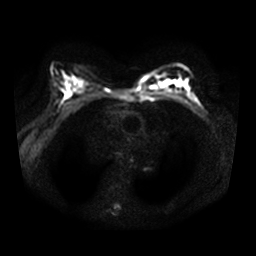
Breast MRI, one axial slice; position 19 of 32 along the scan axis; diffusion-weighted series; image 2 of 4 stored at this slice position (different b-values; order by instance number); 3 T; 256 × 256 image matrix, field of view 340 × 340 mm. Female patient.
Structures marked on this image (expert manual segmentation):
- tumour on diffusion-weighted imaging: bounding box <159,82,169,88> (left, top, right, bottom; pixels)